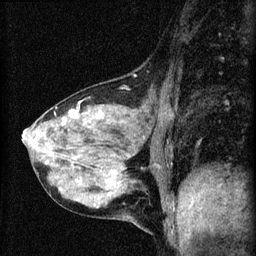
Breast MRI (dynamic contrast-enhanced), one sagittal slice. Slice 21 of 60 in the series (ordered by position). Dynamic contrast-enhanced series, image 2 of 4 at this slice position (ordered by acquisition). 1.5 T. TE 4.2 ms, TR 8.2 ms. 2 mm slice thickness. 256 × 256 image matrix, field of view 180 × 180 mm. Patient: female, 41 years.
Outlined on this slice (semi-automatically segmented with operator editing):
- analysis volume of interest (the breast-tissue region the enhancement analysis was run in; not a lesion): box from (x=23, y=91) to (x=166, y=208) px
- tumour enhancement mask (voxels above the 70 % enhancement threshold inside the analysis volume of interest): (x=23, y=114)–(x=75, y=164)